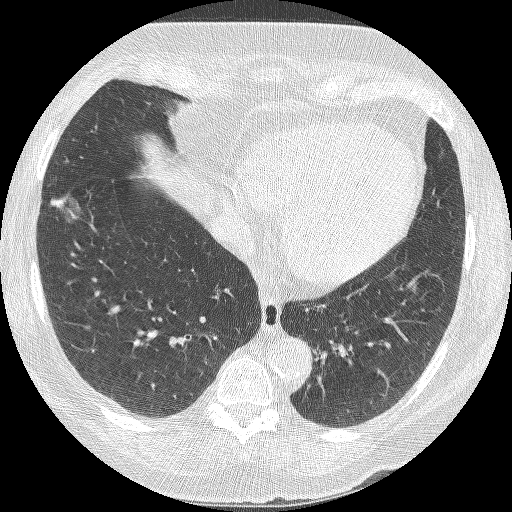
Chest CT (low-dose screening protocol), one axial image; second annual screen; lung window (W 1500 / L -600 HU); lung (sharp) reconstruction kernel (BONE); slice 92 of 245 in the series. Female, age 68 years at enrolment. Current smoker at enrolment.
Expert reader's lesion annotation, bounding box [x1, y1, x2, y2] px = [35, 192, 85, 246]. The exam's reader record, not a measurement of the box and not confirmed to be the same lesion: non-calcified nodule or mass ≥4 mm, right lower lobe, 18 × 15 mm, poorly defined margins, ground glass attenuation, pre-existing on the prior screen: yes; interval growth: yes. Lung cancer was diagnosed 42 days after this screen: bronchiolo-alveolar adenocarcinoma, NOS, right lower lobe, well differentiated (G1), stage IA (AJCC 6th edition), 13 mm at pathology.